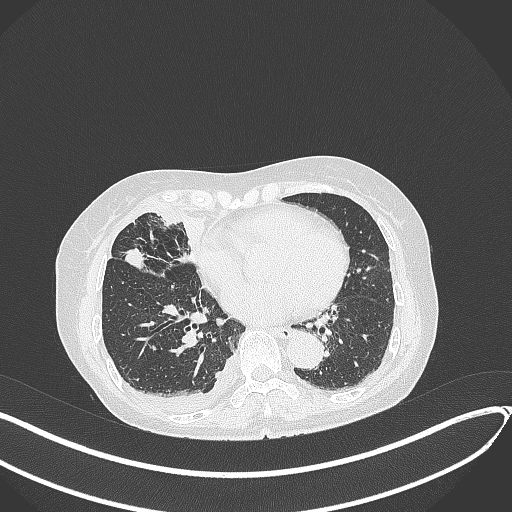
Chest CT, one axial slice; position 157 of 418 along the scan axis; reconstruction kernel B70f; 120 kVp; lung window (W 1500 / L -600 HU); 1 mm slice thickness; 512 × 512 image matrix, field of view 400 × 400 mm. Patient: female, 75 years. From the clinical record (not read from this slice): clinical TNM (as recorded): T2a N3 M0.
Annotated regions visible in this slice (rectangle marked by the reading radiologist):
- lung tumour (recorded histology: adenocarcinoma): bounding box <124,244,153,269> (left, top, right, bottom; pixels)